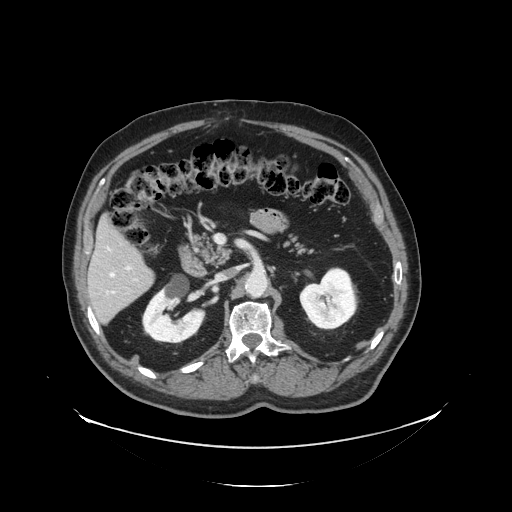
Contrast-enhanced abdominal CT, one axial slice. Slice 64 of 138 in the series (ordered by position). Reconstruction kernel STANDARD. 120 kVp. Intravenous contrast given. Soft-tissue window (W 400 / L 40 HU). 2.5 mm slice thickness. 512 × 512 image matrix, field of view 497 × 497 mm. Male patient, age 77 years. Case-level facts recorded for this patient, not image findings: diagnosis: colorectal cancer liver metastases, imaged before liver resection; multiple liver metastases: no; largest metastasis: 1.5 cm; disease in both lobes: no.
Annotated regions visible in this slice (manually delineated by an expert):
- liver: bounding box [x1, y1, x2, y2] px = [90, 221, 153, 324]
- planned liver remnant (the part of the liver to remain after resection): [90, 221, 146, 286]
- portal vein (with intrahepatic branches): [113, 267, 130, 293]